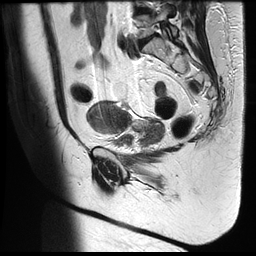
Pelvic MRI for cervical cancer, one sagittal slice. Position 12 of 35 along the scan axis. T2-weighted. 1.5 T. TE 122.8 ms, TR 4992 ms. 4 mm slice thickness. 256 × 256 image matrix, field of view 300 × 300 mm. Female patient, age 42 years.
Annotated regions visible in this slice (expert manual segmentation):
- uterus and cervix: box from (x=87, y=102) to (x=163, y=147) px